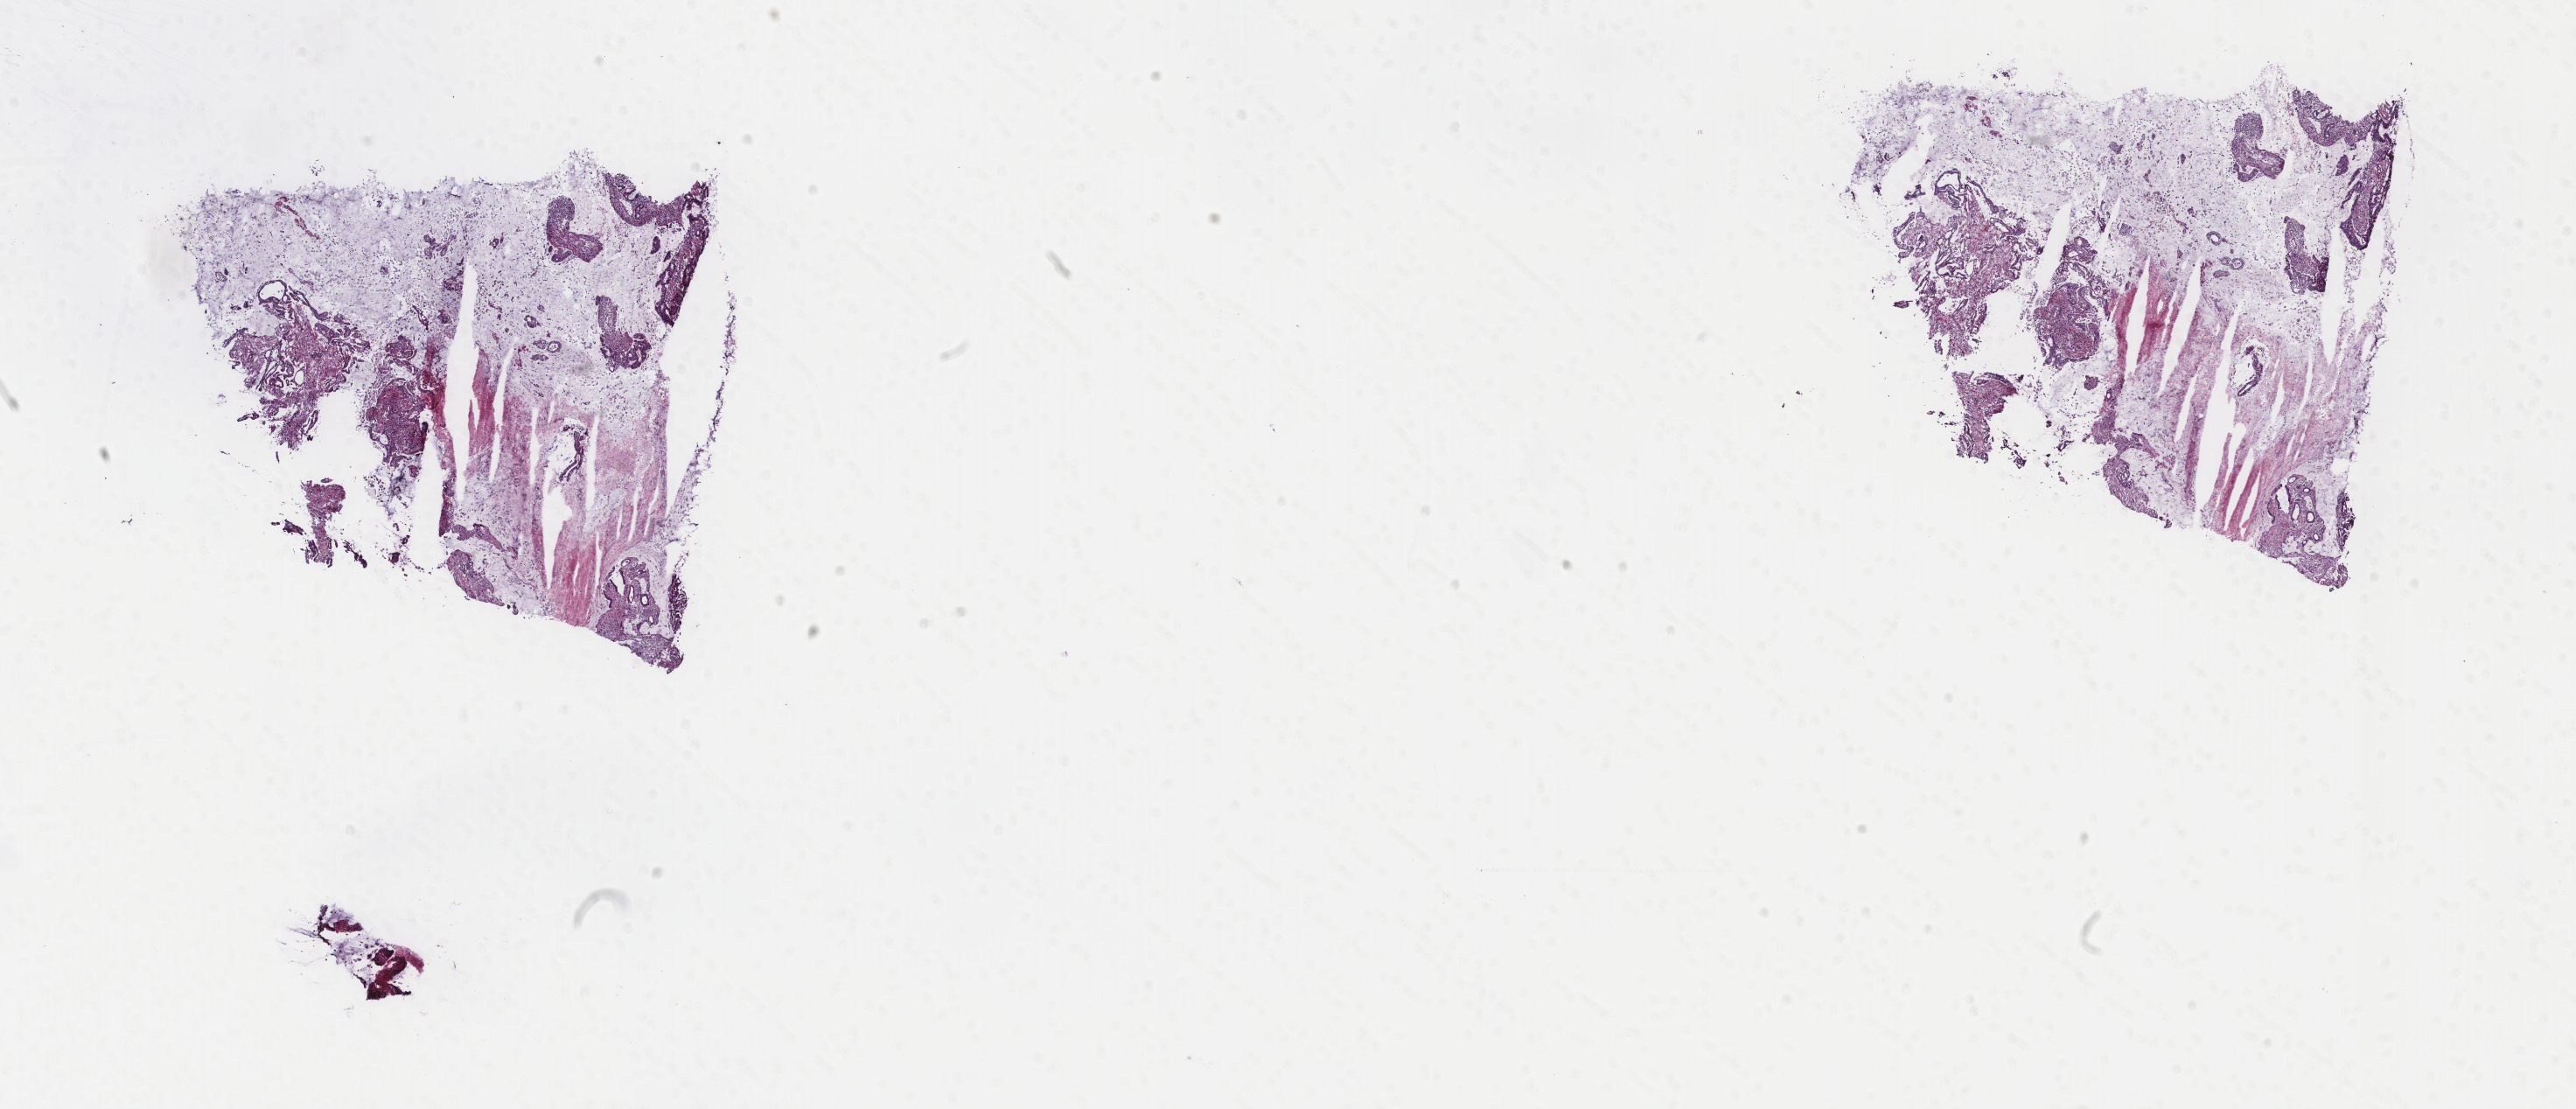
Whole-slide histology image, H&E — shown as a low-resolution overview of the whole scanned area (about 23.4 x 10.1 mm). Frozen section from the top of the tissue portion. Primary tumour sample from the pancreas. Female, age 44 years at initial diagnosis. Histologic grade: G3 (poorly differentiated). Slide review estimates, as recorded: tumour cells 70%, tumour nuclei 70%, normal cells 0%, stromal cells 0%, necrosis 30%. Inflammatory infiltration, as recorded: lymphocyte infiltration 2%, monocyte infiltration 2%, neutrophil infiltration 0%.
Lymph nodes positive (case pathology): 3 of 22 examined. AJCC pathologic stage: IIB (7th edition). Histologic diagnosis: Infiltrating duct carcinoma, NOS.